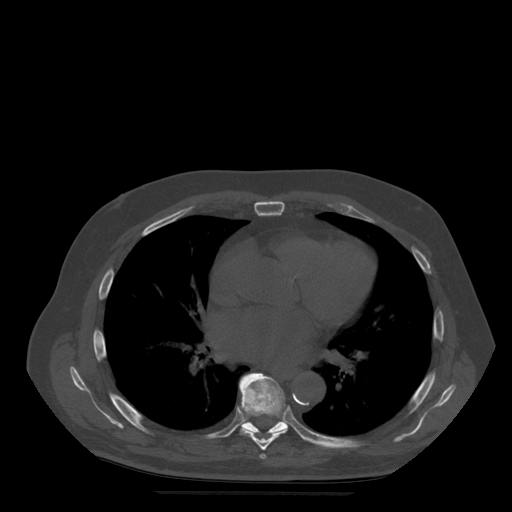
CT including the spine, one axial slice; slice 325 of 522 in the series (ordered by position); bone window (W 1800 / L 400 HU); 1.25 mm slice thickness; 512 × 512 image matrix, field of view 420 × 420 mm. Patient age 72 years. Case-level facts recorded for this patient, not image findings: primary cancer: prostate.
Annotated regions visible in this slice (semi-automatic segmentation, software-assisted and operator-edited):
- T6 vertebra: bounding box (x1, y1, x2, y2) in pixels: (260, 454, 267, 460)
- T7 vertebra: (239, 373, 288, 451)
- T8 vertebra: (240, 373, 309, 442)